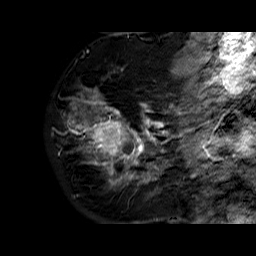
Breast MRI (dynamic contrast-enhanced), one sagittal slice. Position 19 of 60 along the scan axis. Dynamic contrast-enhanced series, time point 2 of 6 at this slice position (early post-contrast). 1.5 T. TE 6.3 ms, TR 32.4 ms. 4 mm slice thickness. 256 × 256 image matrix, field of view 200 × 200 mm. Female patient. From the clinical record (not read from this slice): setting: breast cancer imaged before/during neoadjuvant chemotherapy; receptor status: HR-positive, HER2-negative.
Structures marked on this image (semi-automatically segmented with operator editing):
- analysis volume of interest (the breast-tissue region the enhancement analysis was run in; not a lesion): box from (x=69, y=72) to (x=177, y=183) px
- tumour enhancement mask (voxels above the 100 % enhancement threshold inside the analysis volume of interest): (x=74, y=89)–(x=175, y=183)